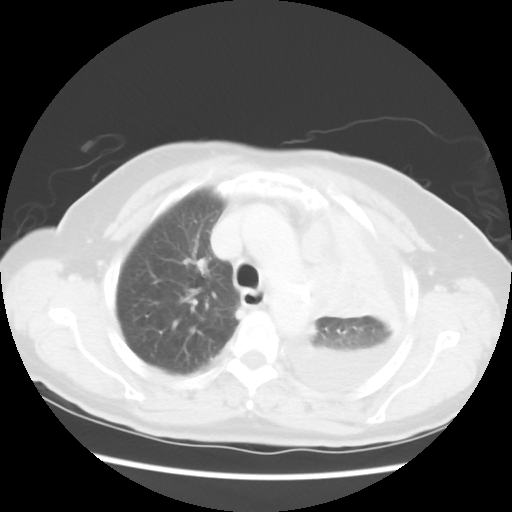
Chest CT, one axial slice. Slice 40 of 52 in the series (ordered by position). Reconstruction kernel STANDARD. 120 kVp. Lung window (W 1500 / L -600 HU). 5 mm slice thickness. 512 × 512 image matrix, field of view 336 × 336 mm. Patient: female, 72 years. From the clinical record (not read from this slice): clinical TNM (as recorded): T4 N3 M1b.
Annotated regions visible in this slice (rectangle marked by the reading radiologist):
- lung tumour (recorded histology: large cell carcinoma): bounding box (x1, y1, x2, y2) in pixels: (306, 262, 373, 327)